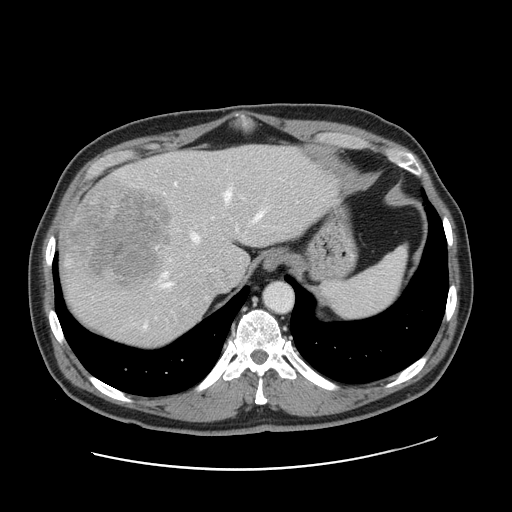
Contrast-enhanced abdominal CT, one axial slice; position 127 of 178 along the scan axis; intravenous contrast given; soft-tissue window (W 400 / L 40 HU); 2.5 mm slice thickness; 512 × 512 image matrix, field of view 403 × 403 mm. Male patient, age 63 years. Case-level facts recorded for this patient, not image findings: diagnosis: colorectal cancer liver metastases, imaged before liver resection; multiple liver metastases: yes; largest metastasis: 8 cm; disease in both lobes: yes.
Annotated regions visible in this slice (expert manual segmentation):
- hepatic veins: bounding box [x1, y1, x2, y2] px = [162, 189, 263, 287]
- liver: [61, 145, 338, 346]
- planned liver remnant (the part of the liver to remain after resection): [150, 146, 338, 279]
- portal vein (with intrahepatic branches): [156, 182, 177, 248]
- liver metastasis: [65, 183, 172, 289]